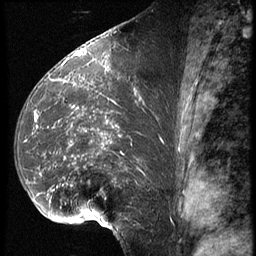
Breast MRI (dynamic contrast-enhanced), one sagittal slice; slice 34 of 62 in the series (ordered by position); 3 images stored at this slice position (order not interpretable as contrast timing); 1.5 T; TE 4.2 ms, TR 9 ms; 2.5 mm slice thickness; 256 × 256 image matrix, field of view 180 × 180 mm. Patient: female, 39 years. Case-level facts recorded for this patient, not image findings: setting: breast cancer imaged before/during neoadjuvant chemotherapy; receptor status: HER2-positive.
Outlined on this slice (semi-automatic segmentation, software-assisted and operator-edited):
- analysis volume of interest (the breast-tissue region the enhancement analysis was run in; not a lesion): bounding box <16,64,162,228> (left, top, right, bottom; pixels)
- tumour enhancement mask (voxels above the 140 % enhancement threshold inside the analysis volume of interest): <41,81,141,197>